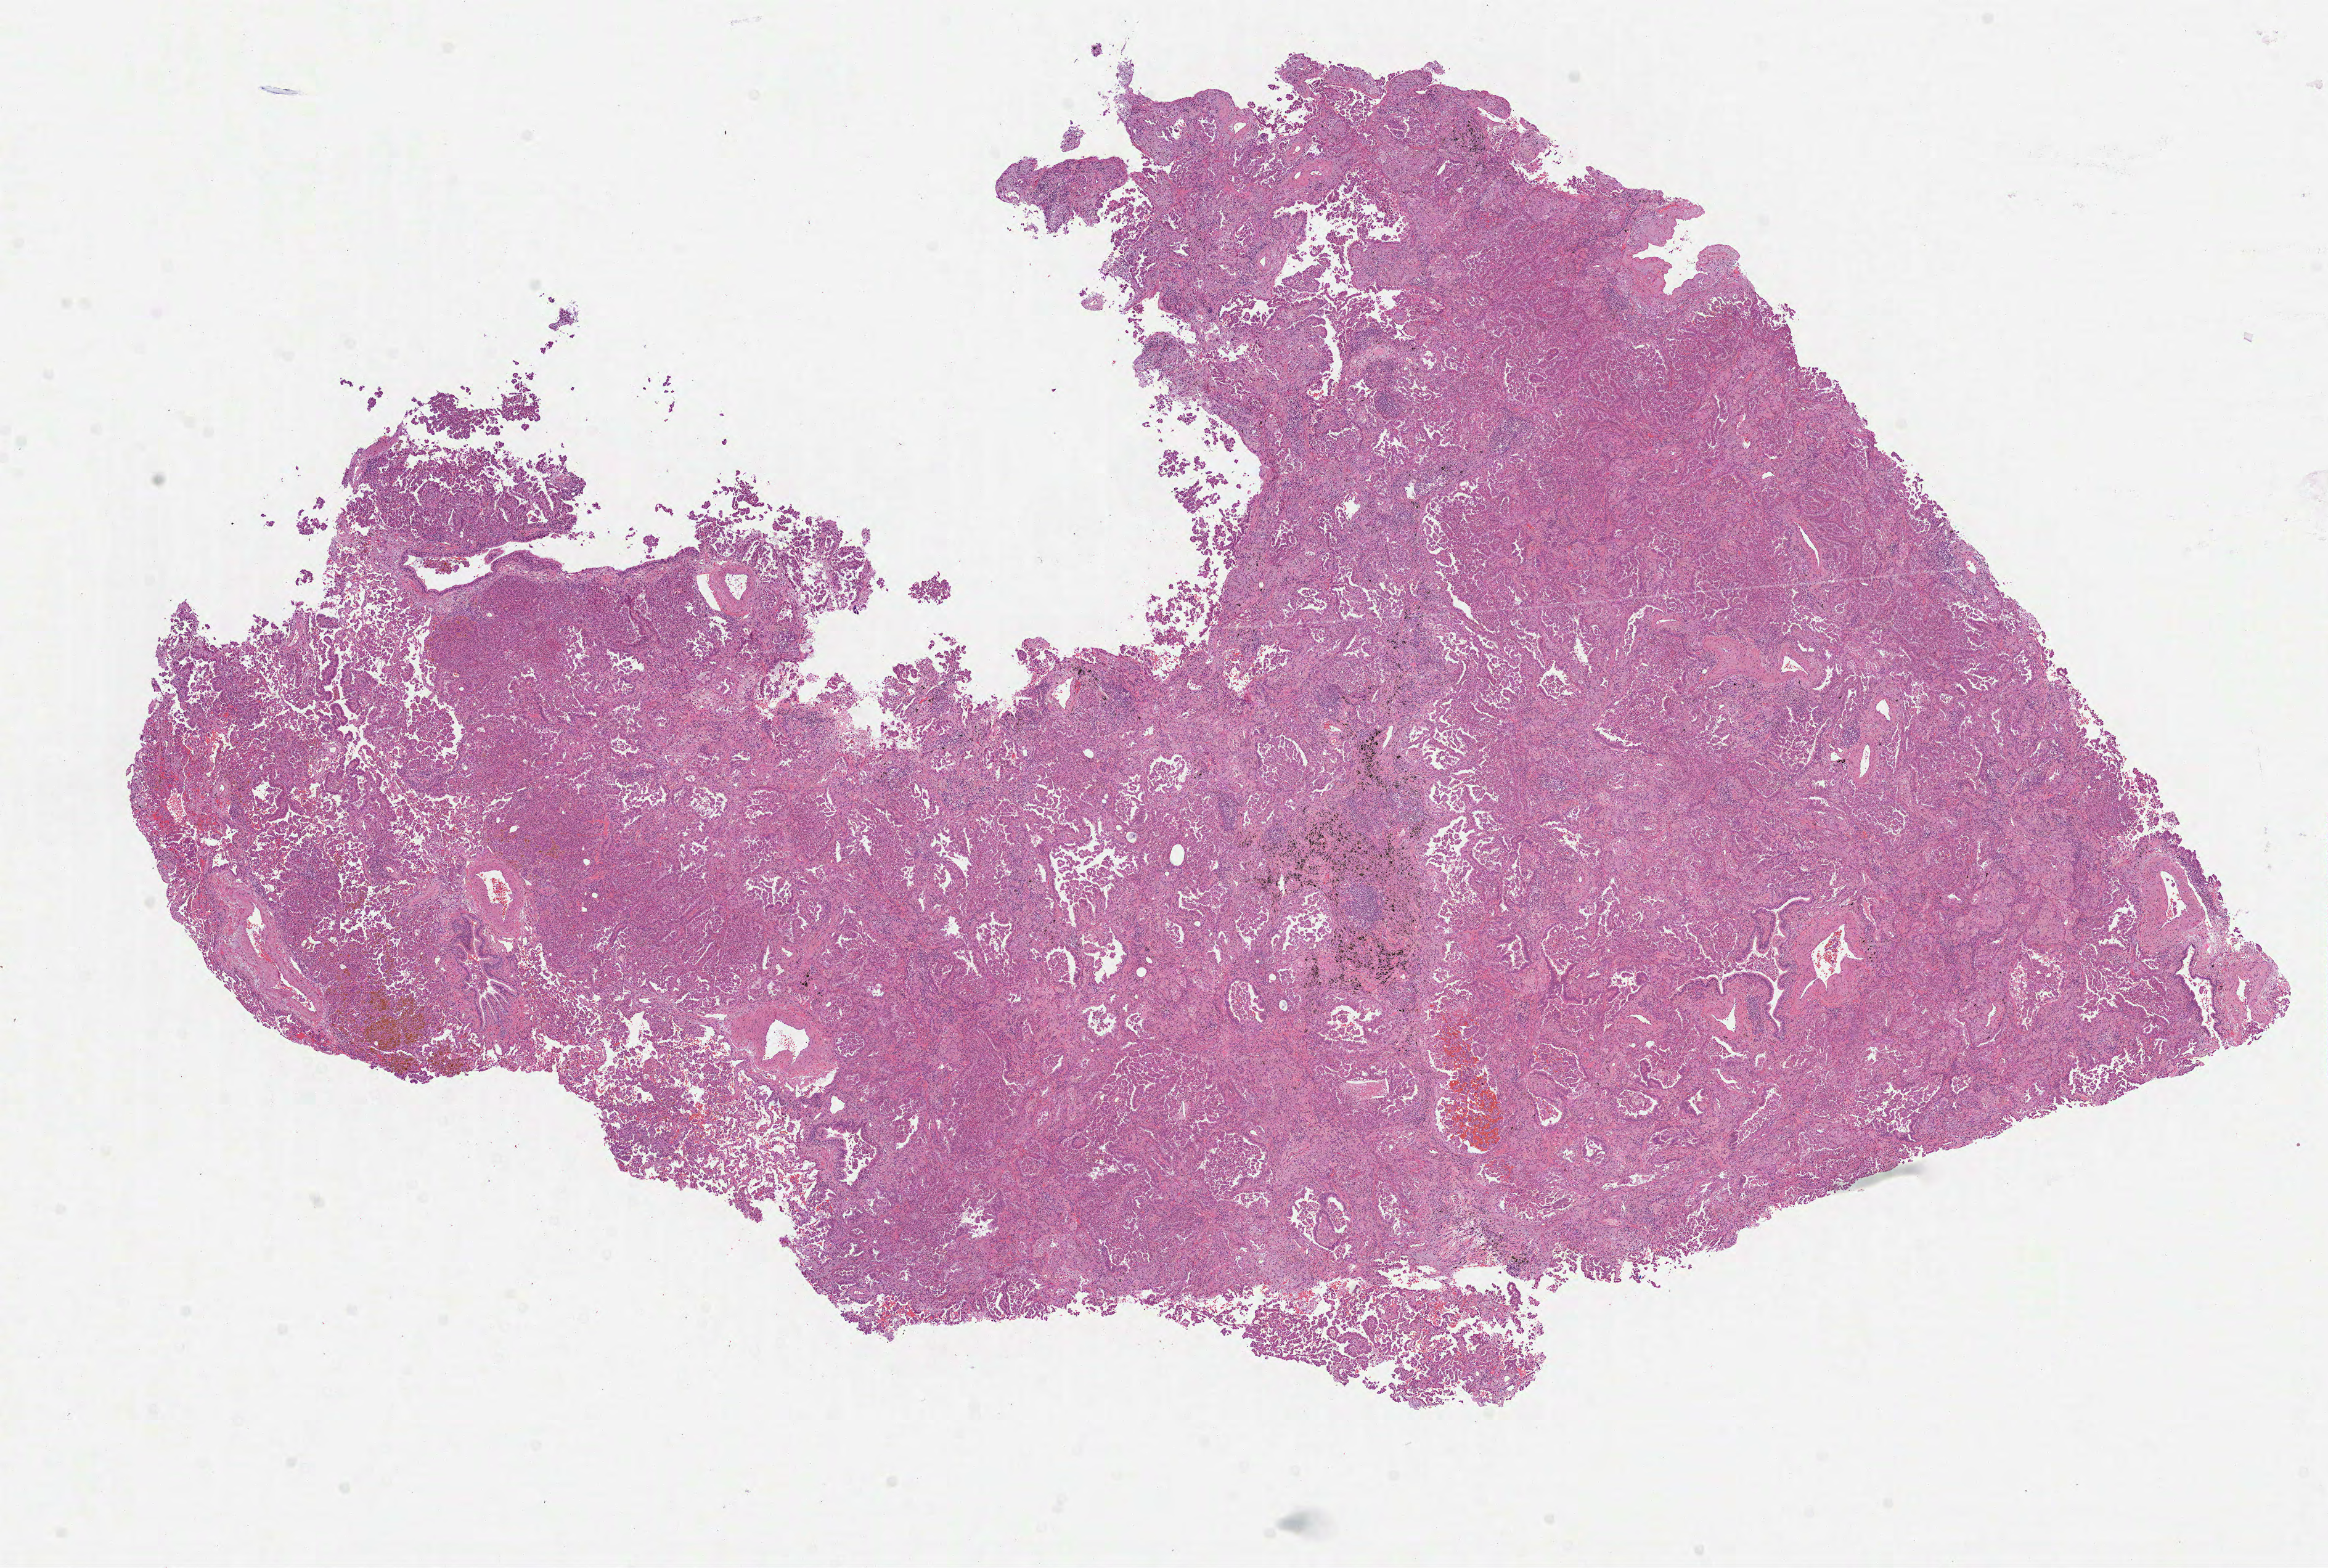
Digitized Hematoxylin and eosin (H&E) stained tissue section (whole slide), low-resolution overview of the scanned area, about 15.2 x 10.3 mm (acquisition: 40x scan), formalin-fixed paraffin-embedded (FFPE) diagnostic section, lung, primary tumour sample. Male patient; age at initial diagnosis 77 years.
- diagnosis: Adenocarcinoma, NOS (lower lobe, lung)
- laterality: right
- AJCC pathologic stage: IIIA